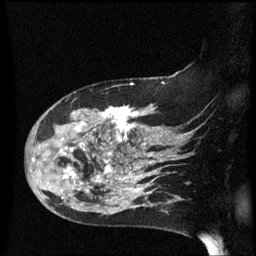
Breast MRI (dynamic contrast-enhanced), one sagittal slice; position 41 of 60 along the scan axis; dynamic contrast-enhanced series, image 2 of 3 at this slice position (ordered by acquisition); 1.5 T; TE 4.2 ms, TR 8.4 ms; 256 × 256 image matrix, field of view 200 × 200 mm. Female patient, age 47 years.
Structures marked on this image (semi-automatically segmented with operator editing):
- analysis volume of interest (the breast-tissue region the enhancement analysis was run in; not a lesion): bounding box (x1, y1, x2, y2) in pixels: (26, 97, 149, 206)
- tumour enhancement mask (voxels above the 70 % enhancement threshold inside the analysis volume of interest): (32, 107, 149, 200)